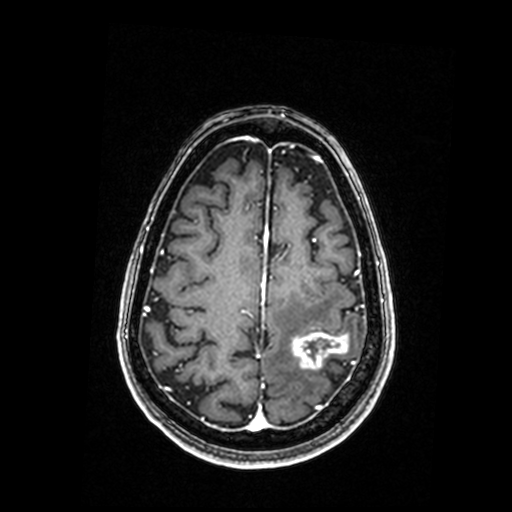
Brain MRI from a brain-tumour surgery series, one axial slice; slice 55 of 192 in the series (ordered by position); T1-weighted post-contrast; 512 × 512 image matrix, field of view 250 × 250 mm. Case-level facts recorded for this patient, not image findings: histopathology: Metastastic Carcinoma, Poorly Differentiated.
Annotated regions visible in this slice (outlined manually by an expert reader):
- tumour: bounding box (x1, y1, x2, y2) in pixels: (292, 332, 348, 368)